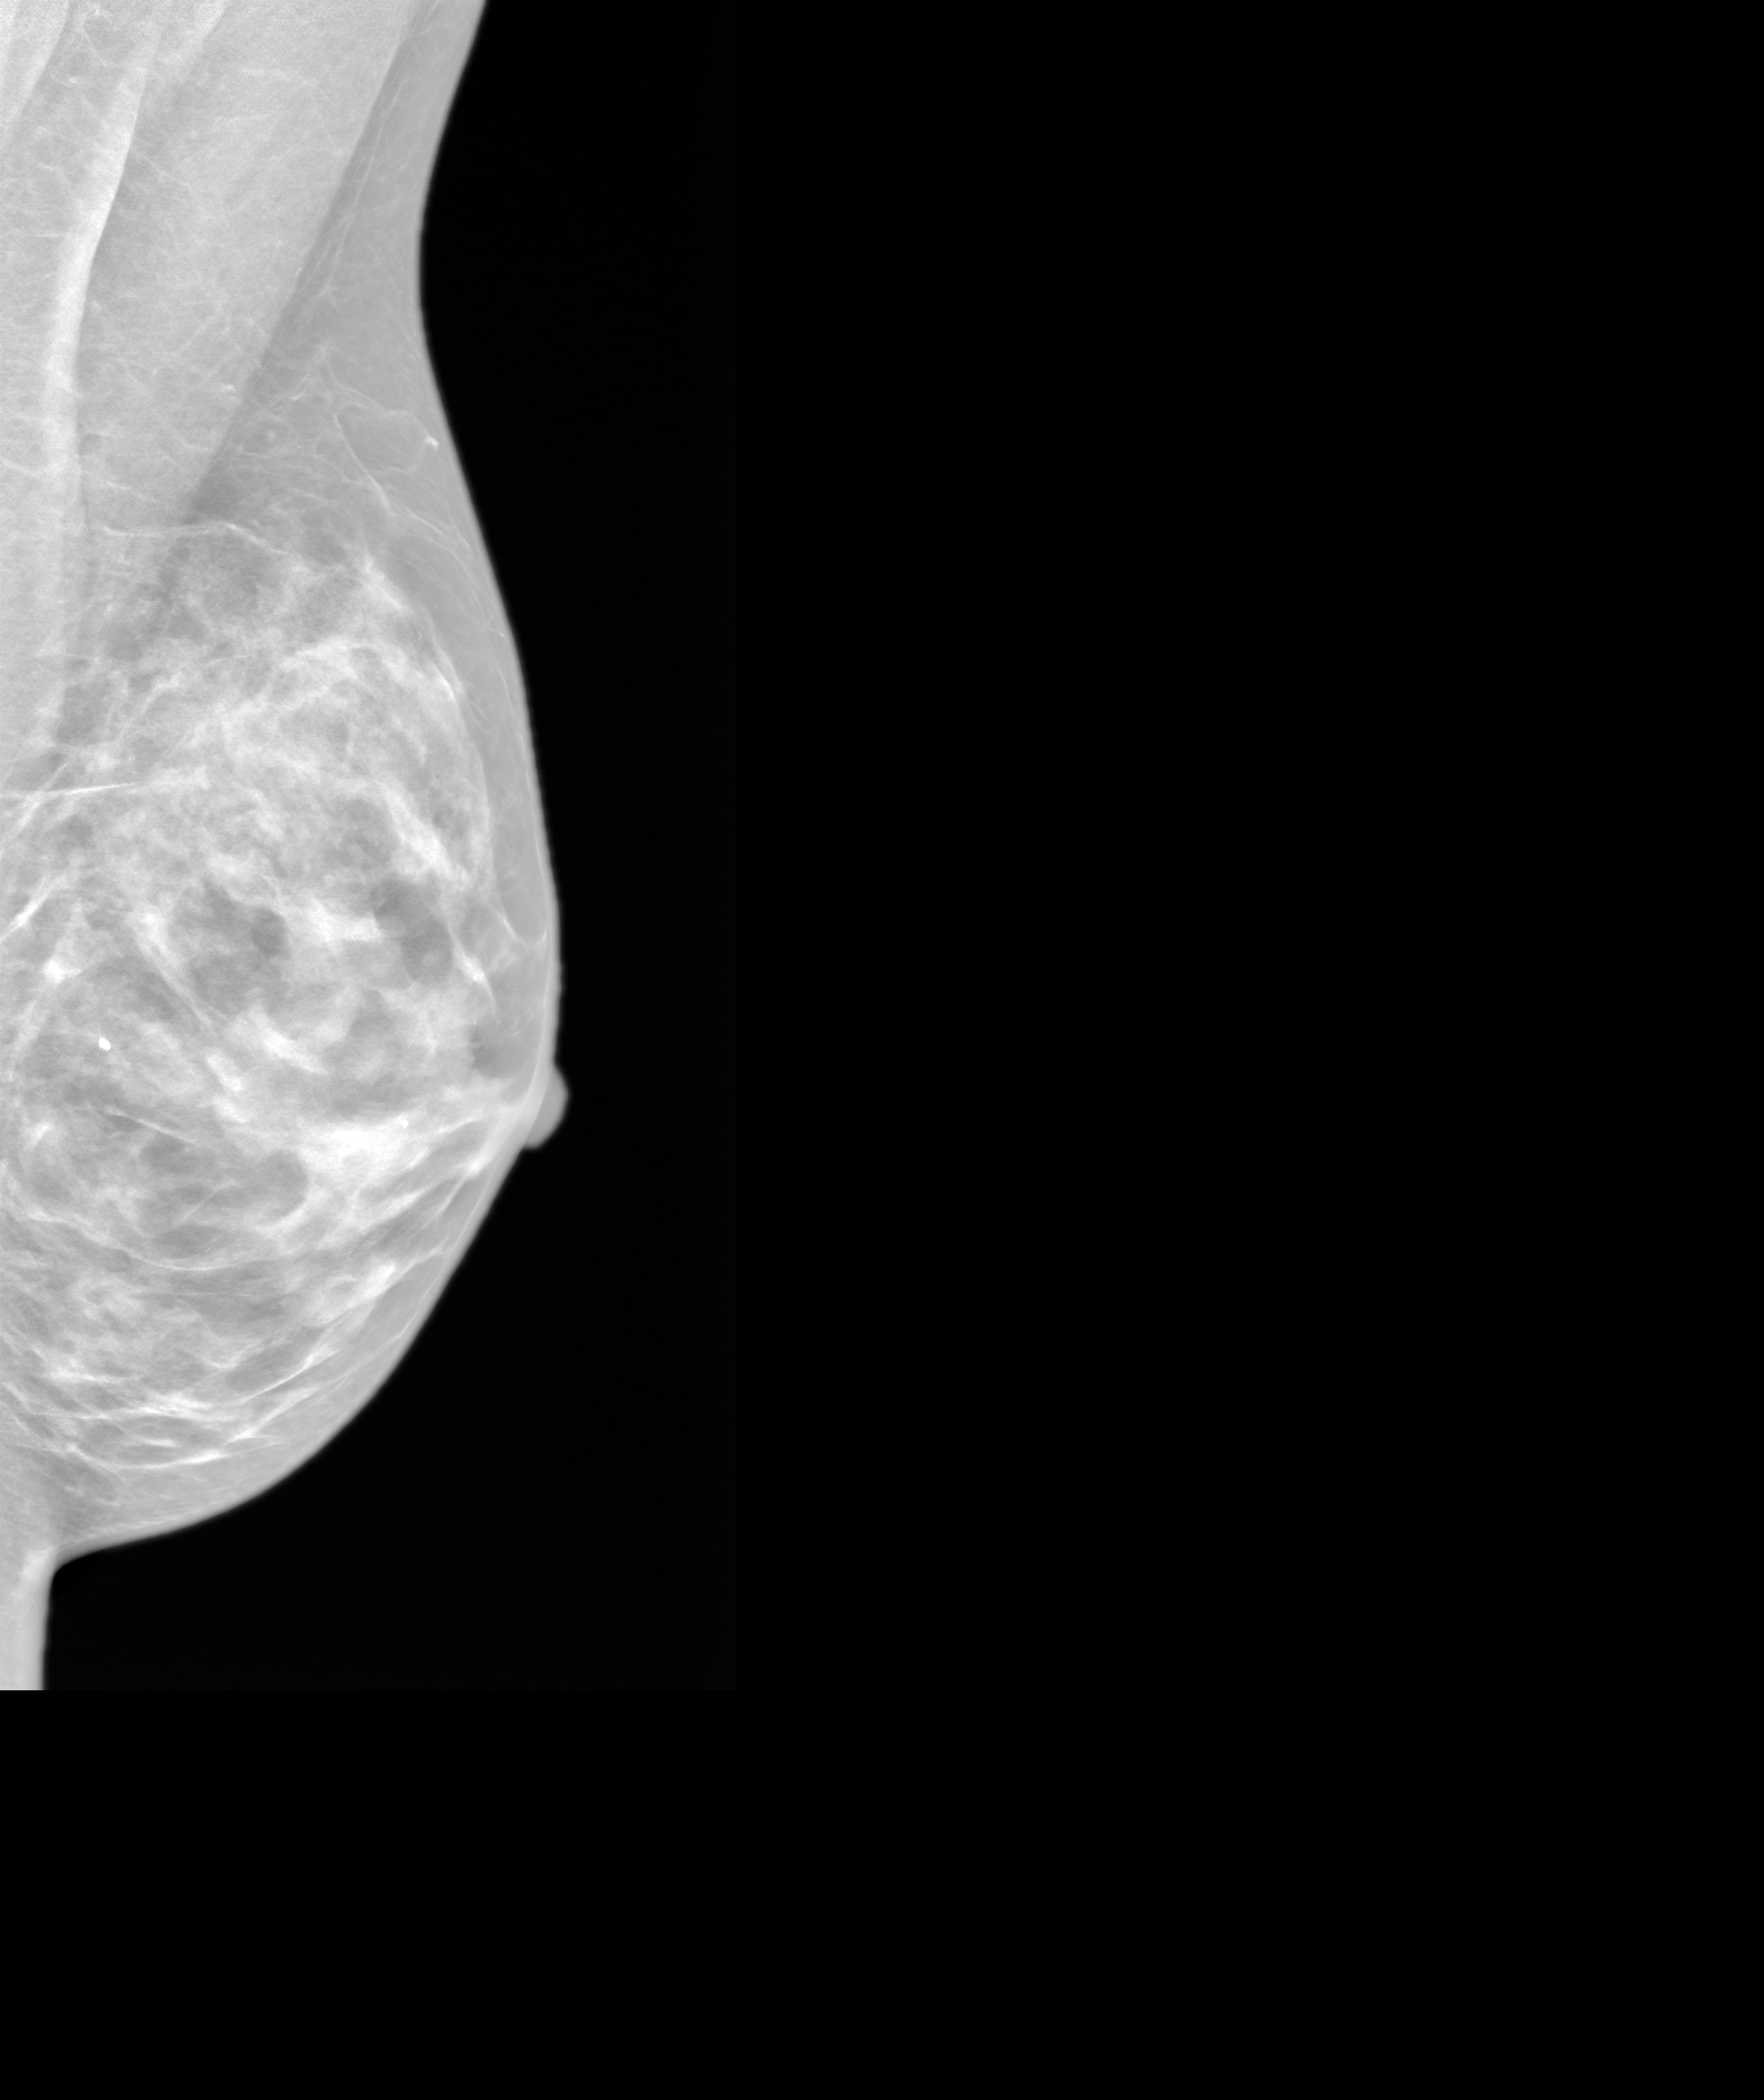
Annual screening mammography examination. Female patient, age 44 years.
Image type: synthesized 2-D view from tomosynthesis. Breast: left. Projection: medio-lateral oblique projection.